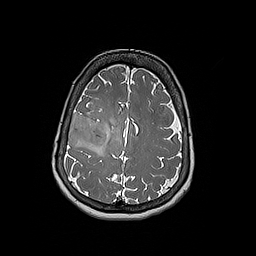
Brain MRI from a brain-tumour surgery series, one axial slice; position 64 of 192 along the scan axis; 1 mm slice thickness; 256 × 256 image matrix. Case-level facts recorded for this patient, not image findings: histopathology: Oligodendroglioma; WHO grade: 3; IDH mutation: yes; tumour location: Right Frontal.
Annotated regions visible in this slice (manually delineated by an expert):
- tumour: box from (x=68, y=112) to (x=108, y=148) px